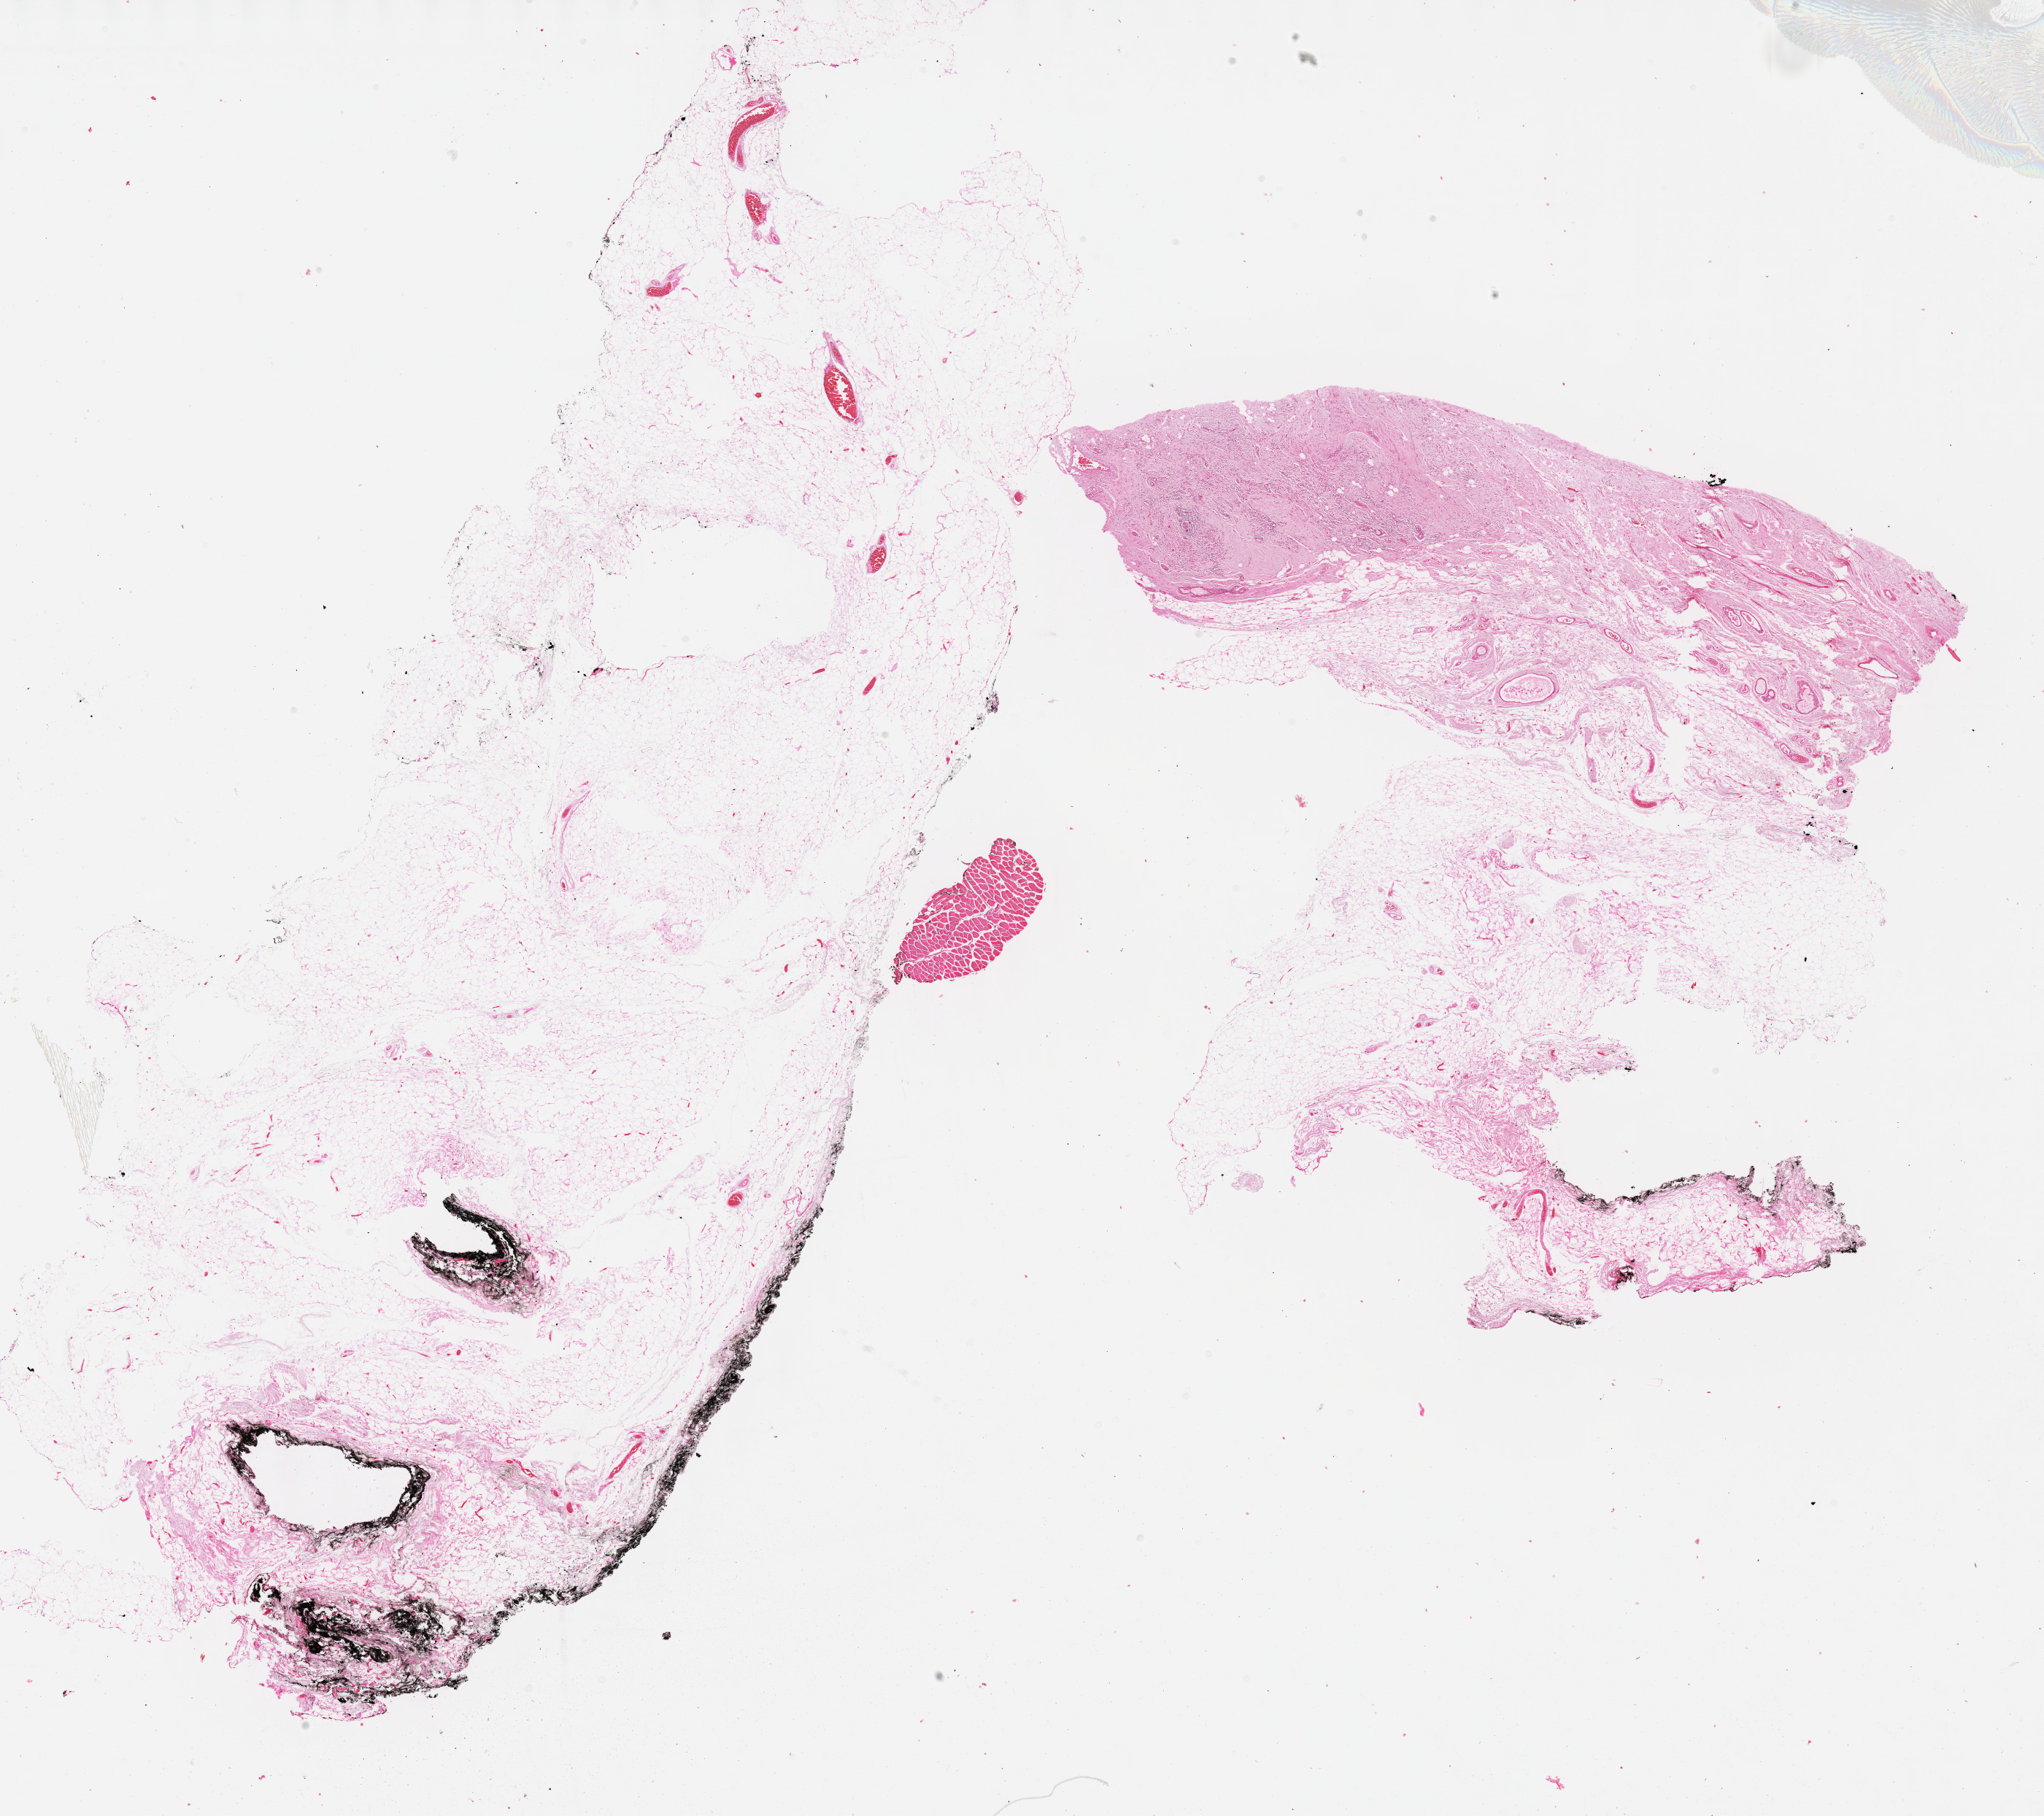
Hematoxylin and eosin (H&E) stained whole-slide image — shown as a low-resolution overview of the whole scanned area (about 22.6 x 20.1 mm, slide scanned at 40x). Formalin-fixed paraffin-embedded (FFPE) diagnostic section. Breast, primary tumour sample. Female, age 63 years at initial diagnosis.
AJCC pathologic stage: IV. Diagnosis: Lobular carcinoma, NOS. Lymph nodes positive (case pathology): 0 of 1 examined. TNM: T2 N0 M1.